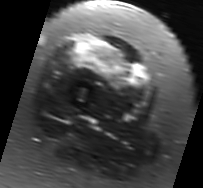
MRI of an extremity soft-tissue mass, one axial slice; position 22 of 91 along the scan axis; T2-weighted fat-saturated; MR volume resampled by the dataset authors to the PET/CT grid (not the native acquisition matrix); 3.27 mm slice thickness; 203 × 188 image matrix, field of view 198 × 184 mm. Female patient. From the clinical record (not read from this slice): histological type: malignant solitary fibrous tumor; grade: intermediate; site of the primary tumour: right thigh.
Outlined on this slice (expert contour drawn on MRI and transferred to this co-registered scan by the dataset authors):
- gross tumour volume including surrounding oedema: bounding box (x1, y1, x2, y2) in pixels: (69, 35, 150, 98)